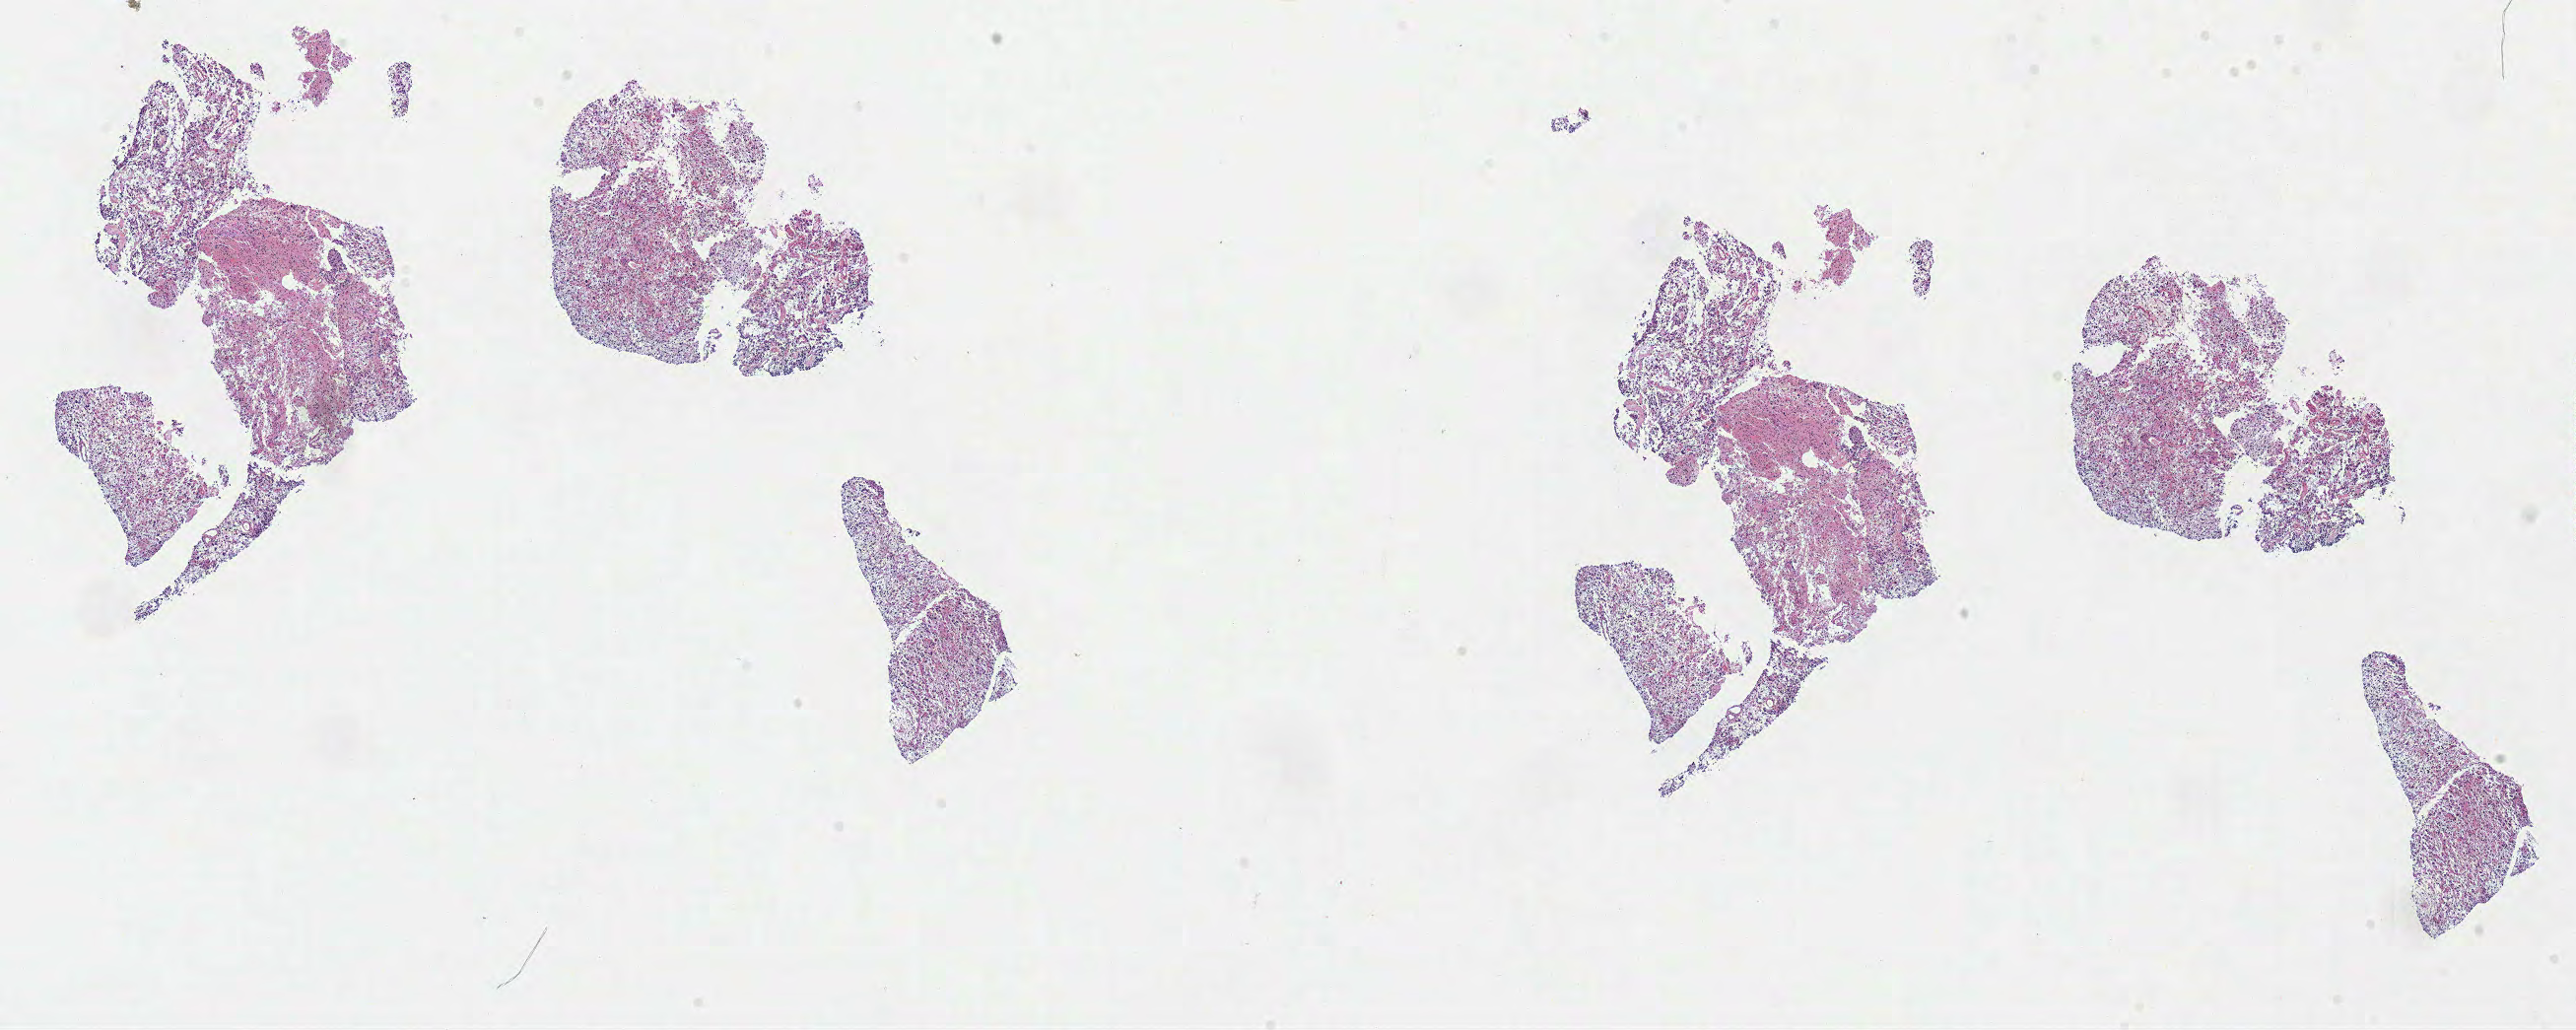
Digitized Hematoxylin and eosin (H&E) stained tissue section (whole slide) — shown as a low-resolution overview of the whole scanned area (about 20.6 x 8.2 mm), frozen section from the top of the tissue portion, sample: primary tumour, brain. Female patient; age at initial diagnosis 35 years. Histologic grade: G3 (poorly differentiated). Slide review estimates, as recorded: tumour cells 100%, tumour nuclei 80%, normal cells 0%, stromal cells 0%, necrosis 0%.
- diagnosis: Astrocytoma, anaplastic (cerebrum)
- laterality: right